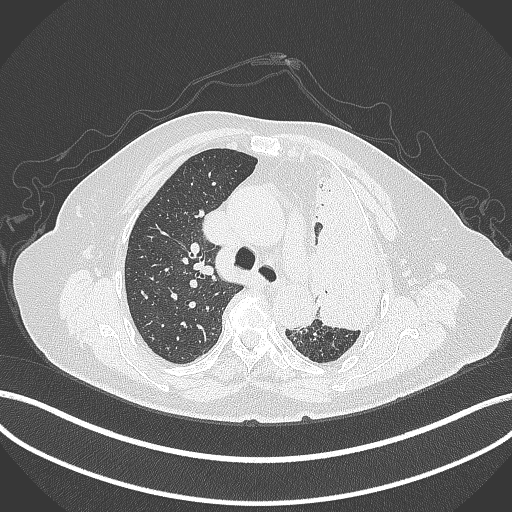
Chest CT, one axial slice. Slice 274 of 399 in the series (ordered by position). Reconstruction kernel B70f. Lung window (W 1500 / L -600 HU). 512 × 512 image matrix, field of view 400 × 400 mm. Patient: female, 75 years. Case-level facts recorded for this patient, not image findings: clinical TNM (as recorded): T3 N3 M1.
Annotated regions visible in this slice (bounding box drawn by a radiologist):
- lung tumour (recorded histology: adenocarcinoma): bounding box (x1, y1, x2, y2) in pixels: (299, 146, 390, 333)